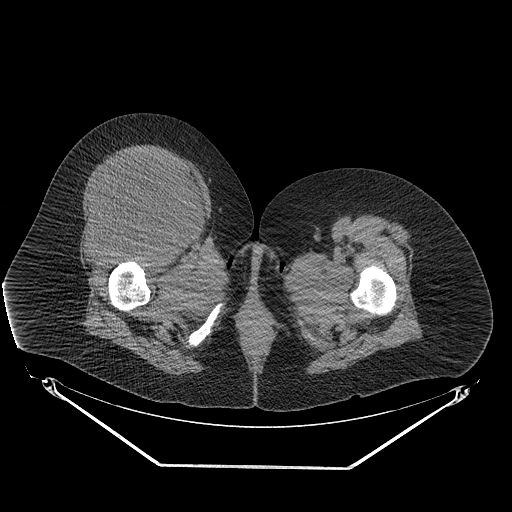
CT of an extremity soft-tissue mass (from a PET/CT study), one axial slice; slice 51 of 267 in the series (ordered by position); reconstruction kernel STANDARD; 140 kVp; soft-tissue window (W 400 / L 40 HU); 3.75 mm slice thickness; 512 × 512 image matrix, field of view 500 × 500 mm. Female patient. Case-level facts recorded for this patient, not image findings: histological type: malignant solitary fibrous tumor; grade: intermediate; site of the primary tumour: right thigh.
Structures marked on this image (expert contour drawn on MRI and transferred to this co-registered scan by the dataset authors):
- gross tumour volume including surrounding oedema: box from (x=77, y=153) to (x=202, y=245) px
- gross tumour volume (mass): (x=80, y=153)–(x=199, y=243)